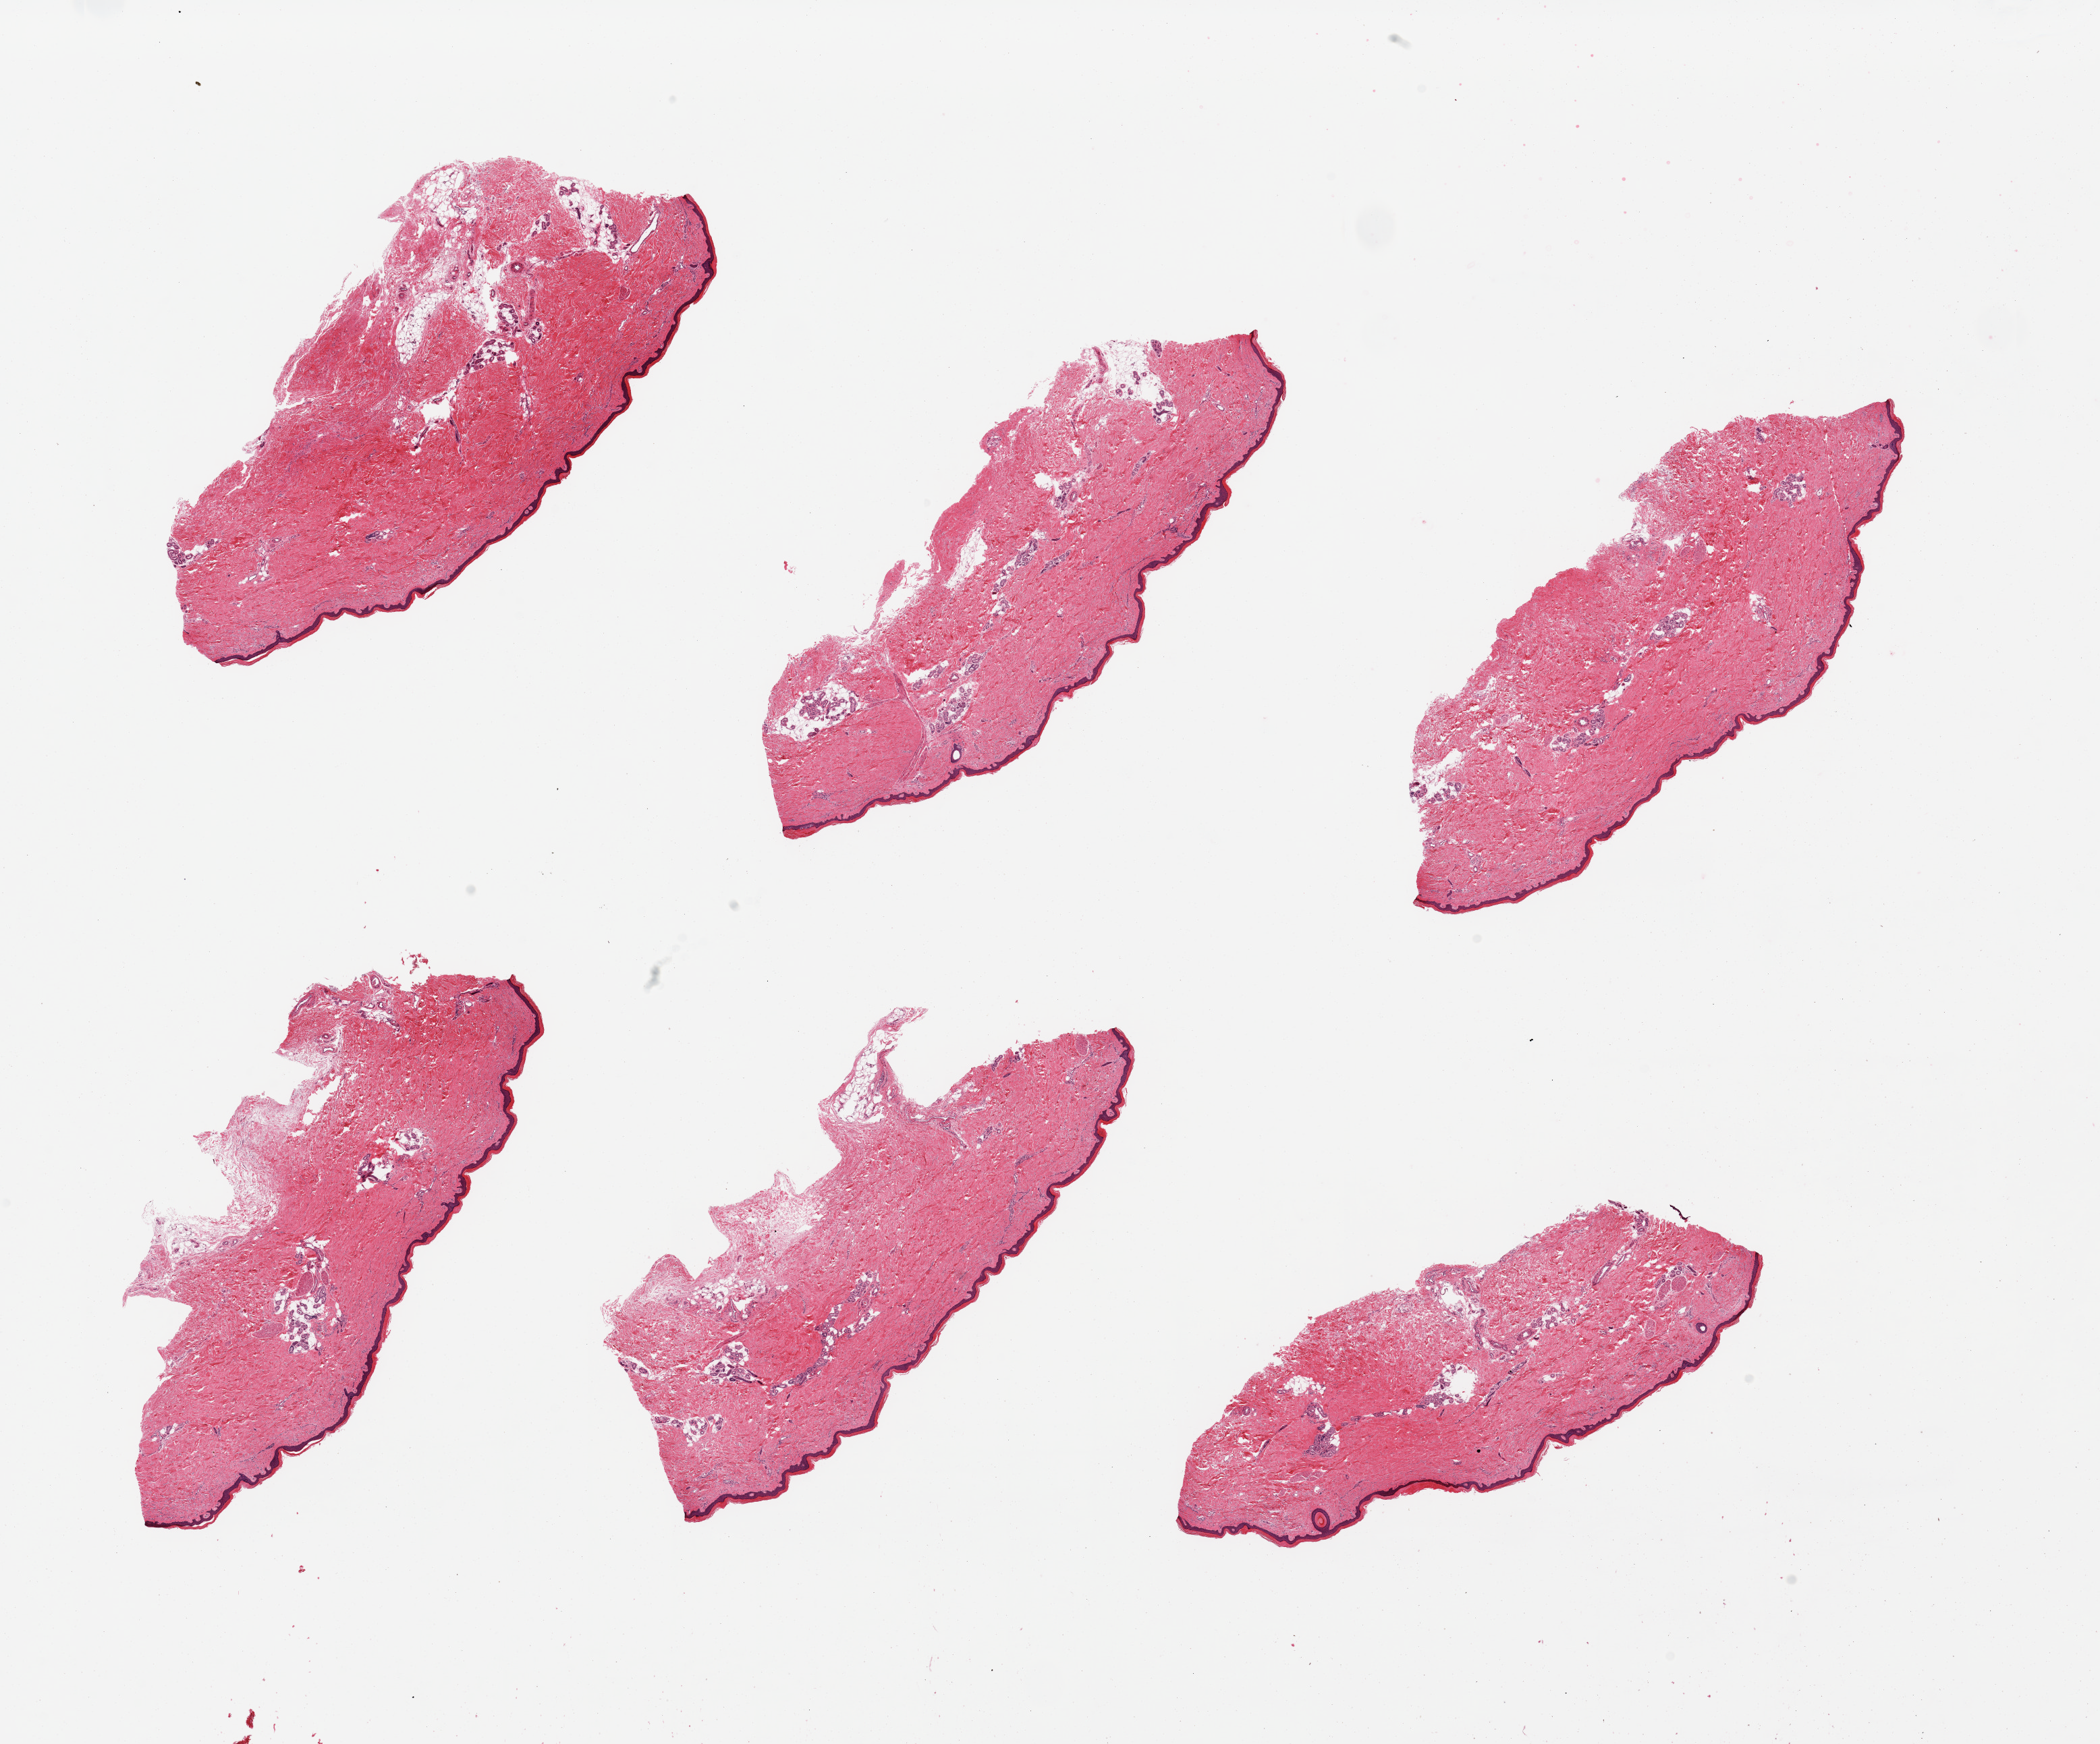
Hematoxylin and eosin (H&E) whole-slide image — shown as a low-resolution overview of the whole scanned area (about 24.6 x 20.4 mm, slide scanned at 20x), PAXgene-fixed paraffin-embedded (PFPE) section, section of skin of lower leg (target tissue), tissue donor sample. Male donor.
* review note (as recorded): 6 pieces, no significant dermal fat; squamous epithelium is ~40-50 microns